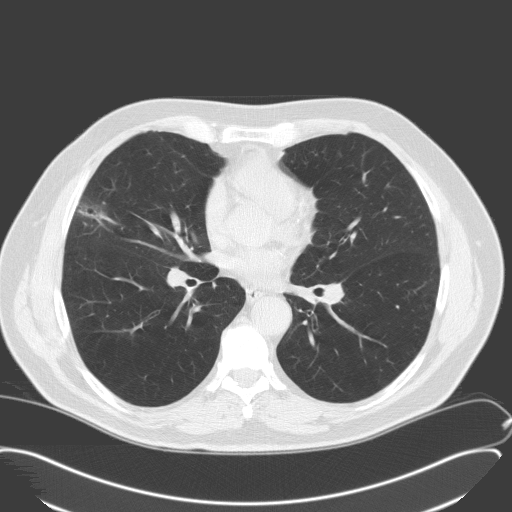
Chest CT (low-dose screening protocol), one axial image. Second annual screen. Lung window (W 1500 / L -600 HU). 3.2 mm slice thickness. 512 × 512 image matrix, field of view 400 × 400 mm. Male, age 65 years at enrolment. Former smoker at enrolment.
- Lesion marked by an expert reader, bounding box [x1, y1, x2, y2] px = [57, 192, 116, 245].
- Screening reader's record for this exam: no non-calcified nodule ≥4 mm recorded.
- Official screen result: negative screen, minor abnormalities not suspicious for lung cancer.
- Lung cancer was diagnosed 346 days after this screen: adenocarcinoma, NOS, right middle lobe, moderately differentiated (G2), stage IA (AJCC 6th edition), 25 mm at pathology.